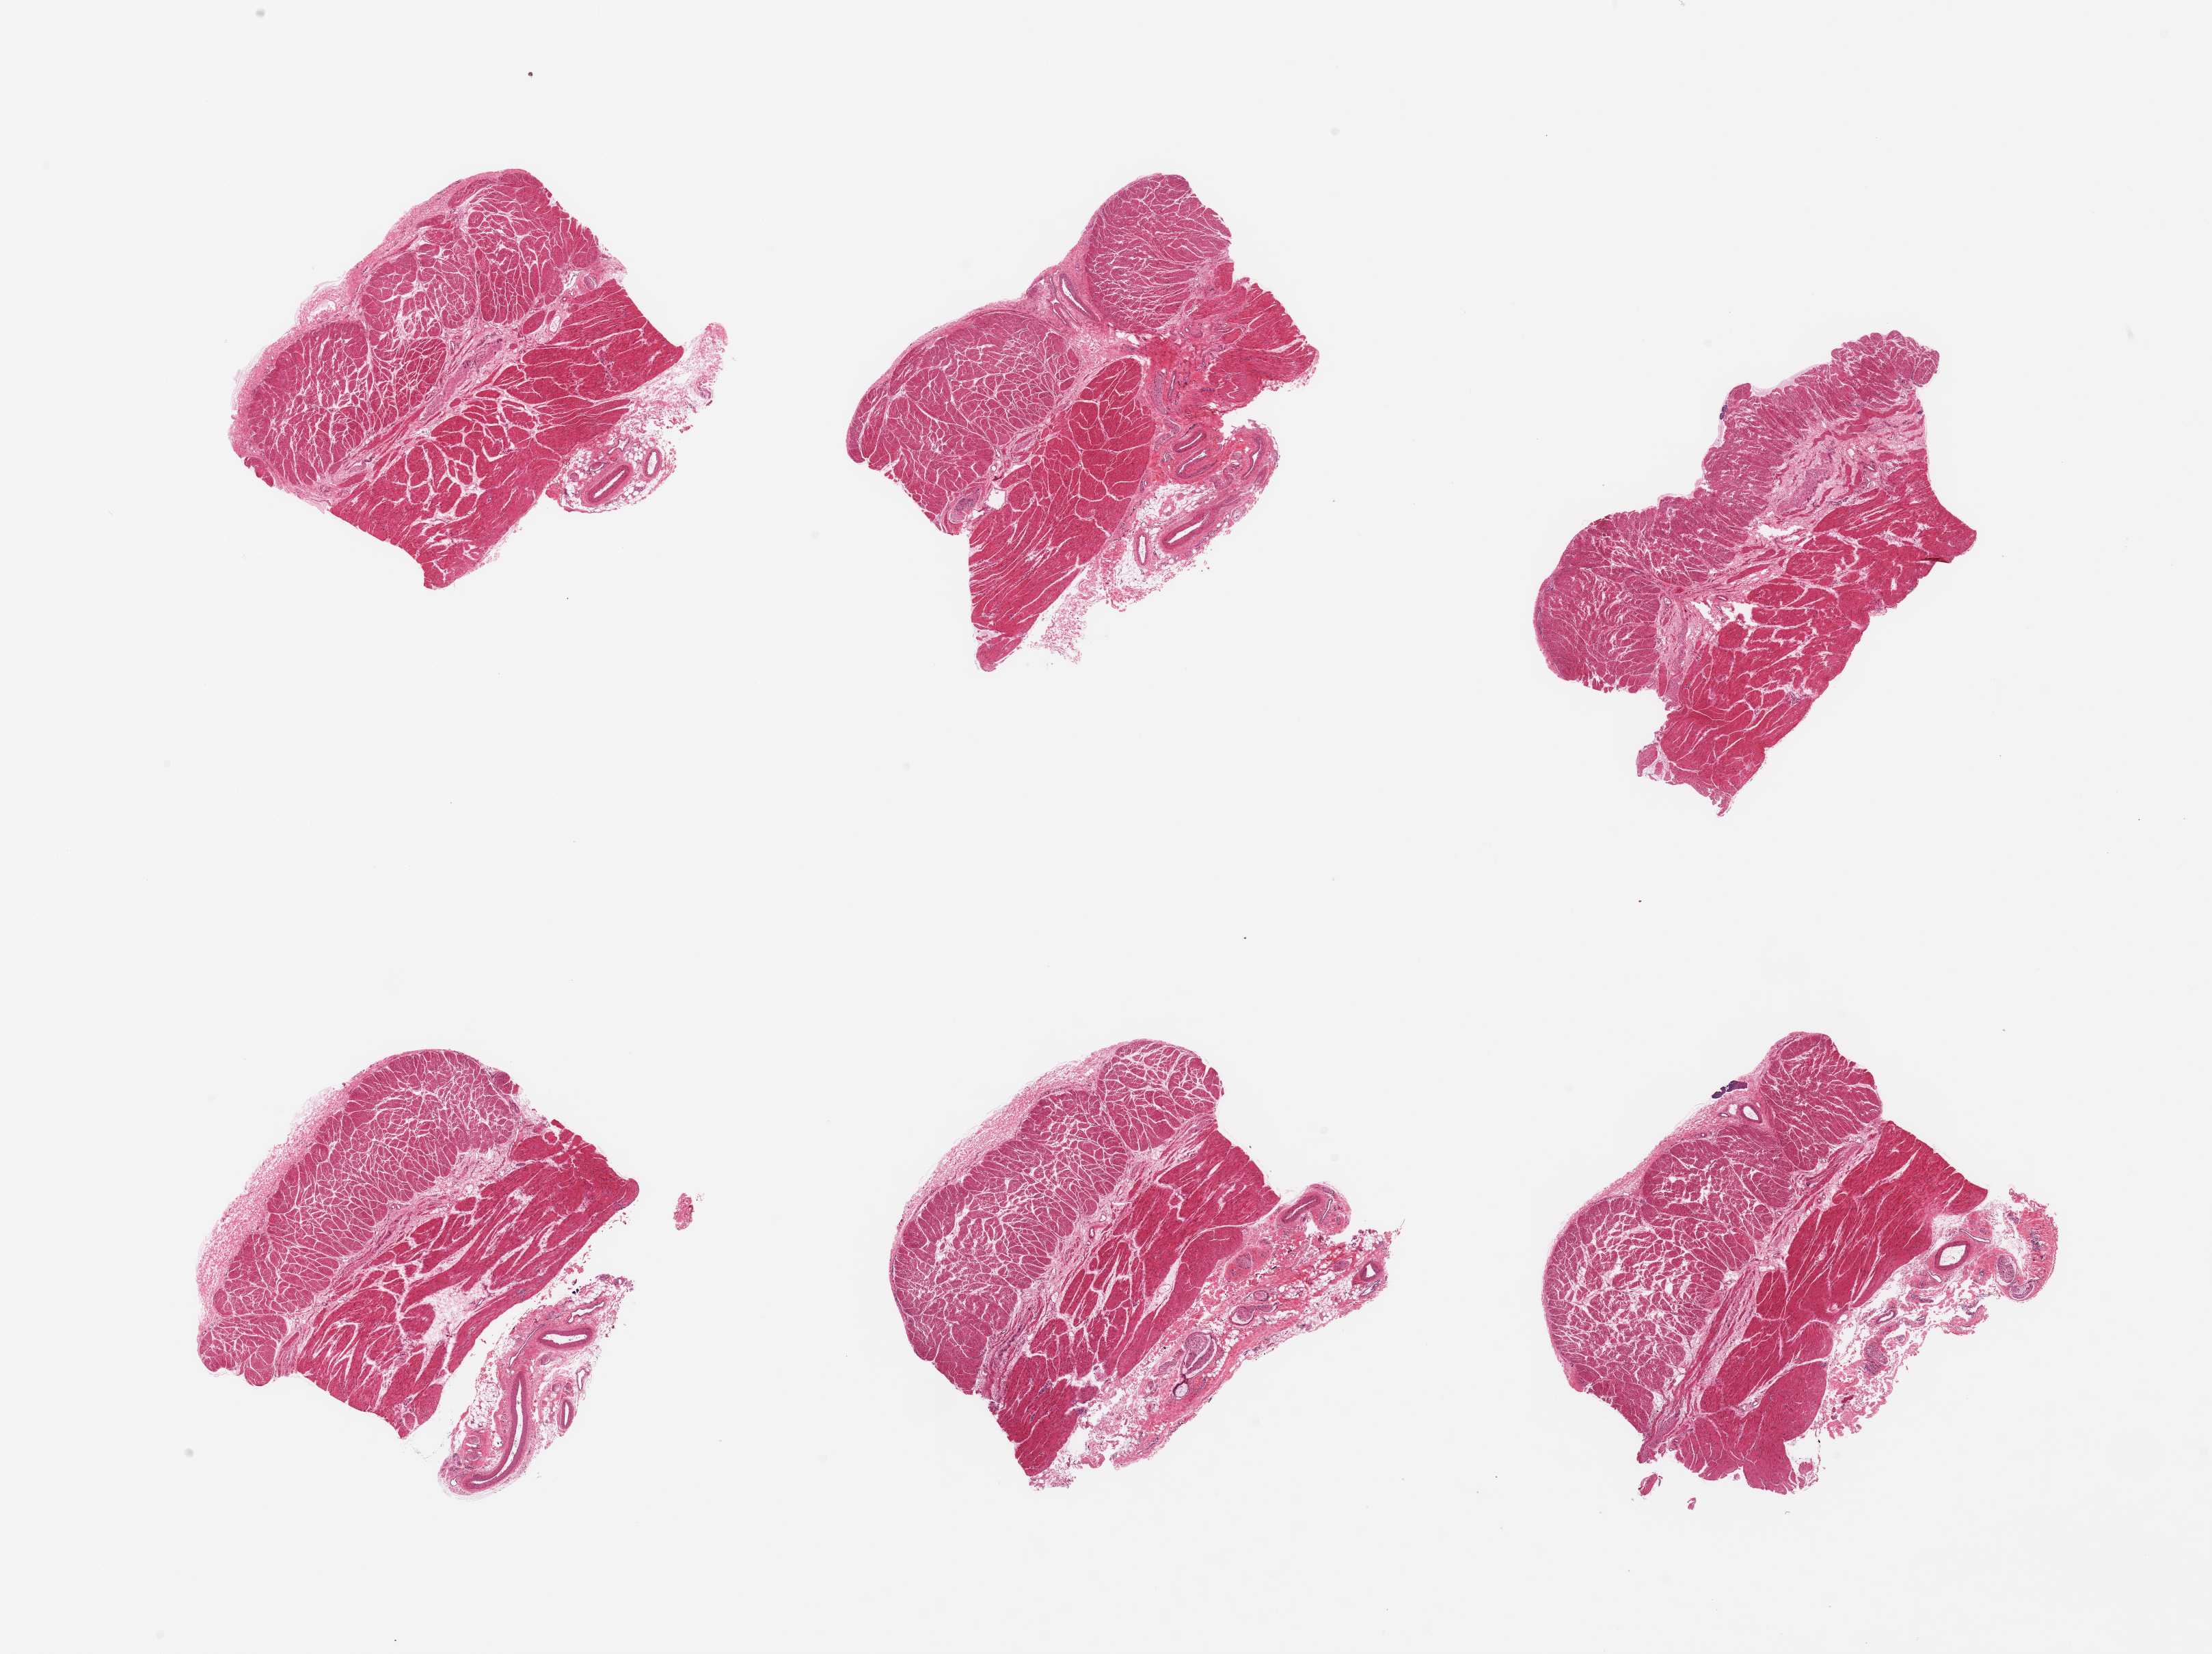
Whole-slide image, H&E stain — shown as a low-resolution overview of the whole scanned area (about 25.6 x 19.1 mm, acquisition: 20x scan); PAXgene-fixed paraffin-embedded (PFPE) section; sampled site (target tissue): esophageal muscle; donor tissue sample. Donor: female.
Review note (as recorded): 6 pieces, confirmed target muscularis.